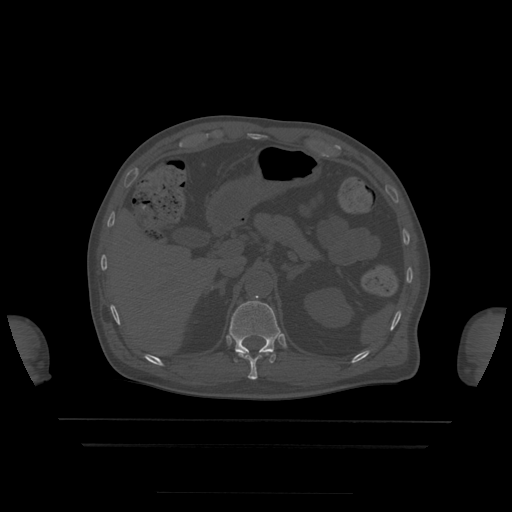
CT including the spine, one axial slice; bone window (W 1800 / L 400 HU); 1.25 mm slice thickness; 512 × 512 image matrix. Patient age 68 years. Case-level facts recorded for this patient, not image findings: primary cancer: urothelial.
Annotated regions visible in this slice (semi-automatically segmented with operator editing):
- T11 vertebra: bounding box (x1, y1, x2, y2) in pixels: (239, 351, 275, 380)
- T12 vertebra: (229, 296, 281, 359)